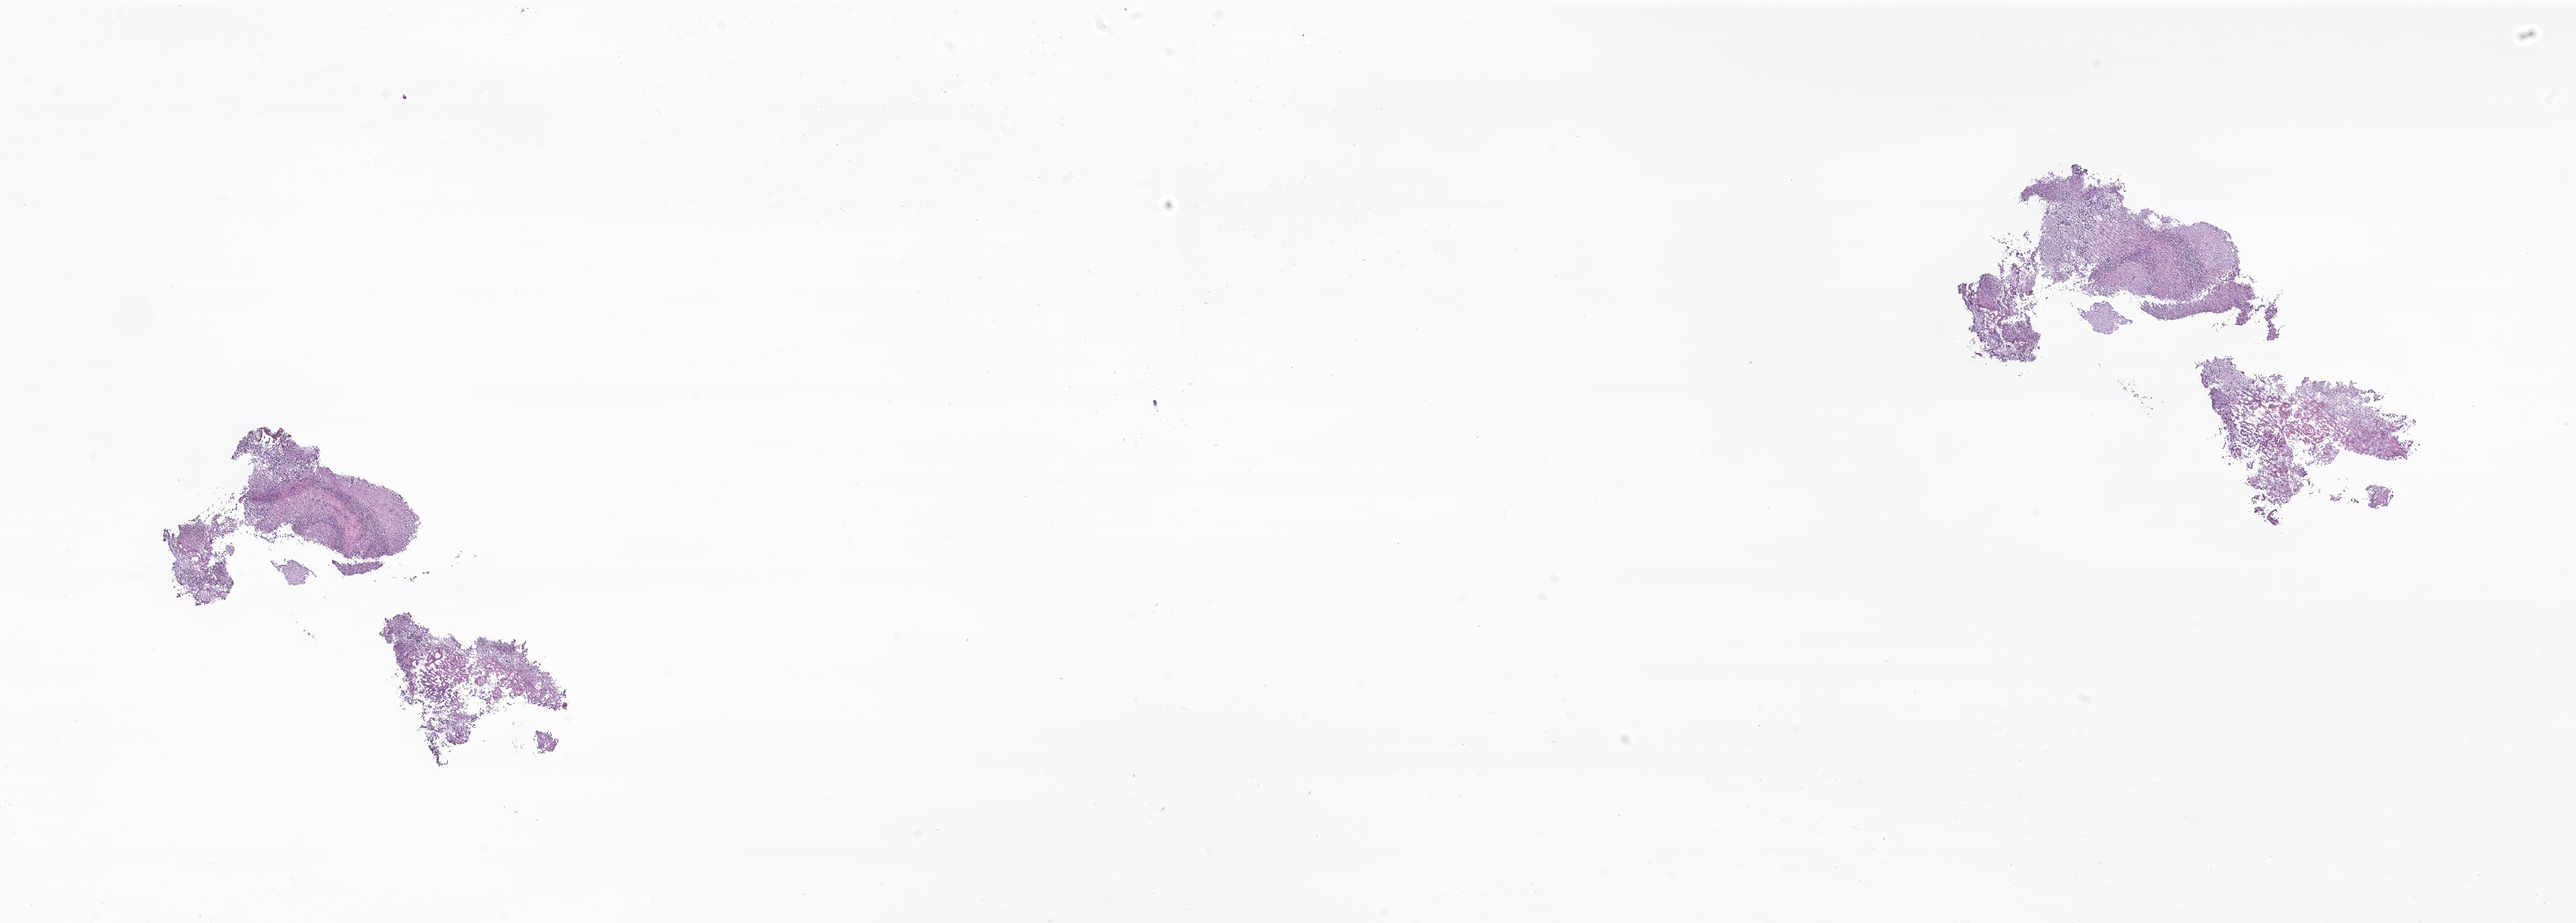
Haematoxylin and eosin whole-slide image of tumor tissue from the cerebellum — shown as a low-resolution overview of the whole scanned area (about 29.6 x 10.6 mm); cryosection (OCT / tissue freezing medium). Patient: female, age 211 months.
Diagnosis: Medulloblastoma, NOS.